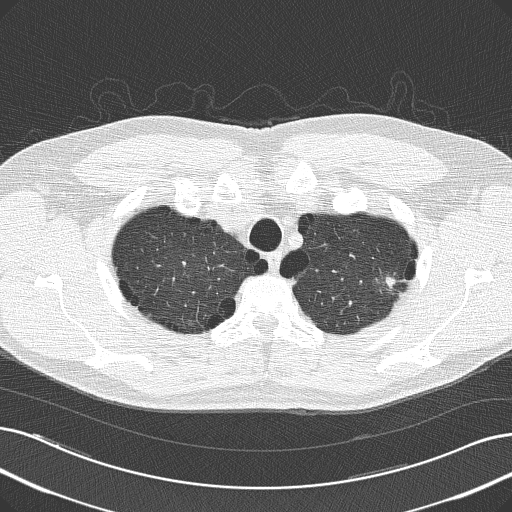
Low-dose screening chest CT, axial slice. Baseline screening round. Lung window (W 1500 / L -600 HU). 2 mm slice thickness. Lung (sharp) reconstruction kernel (B50f). Male, age 62 years at enrolment. Current smoker at enrolment.
• Lesion marked by an expert reader, bounding box (x1, y1, x2, y2) in pixels: (364, 259, 416, 307).
• The screening reader recorded 4 non-calcified nodules or masses ≥4 mm on this exam (left upper lobe, right upper lobe, right upper lobe, right middle lobe); which of them this box marks is not recorded.
• Official screen result: positive, change unspecified: nodule(s) >= 4 mm or enlarging nodule(s), mass(es), or other non-specific abnormalities suspicious for lung cancer.
• Participant outcome: lung cancer diagnosed 383 days after this screen — adenocarcinoma, NOS, left upper lobe, well differentiated (G1), stage IB (AJCC 6th edition), 17 mm at pathology.